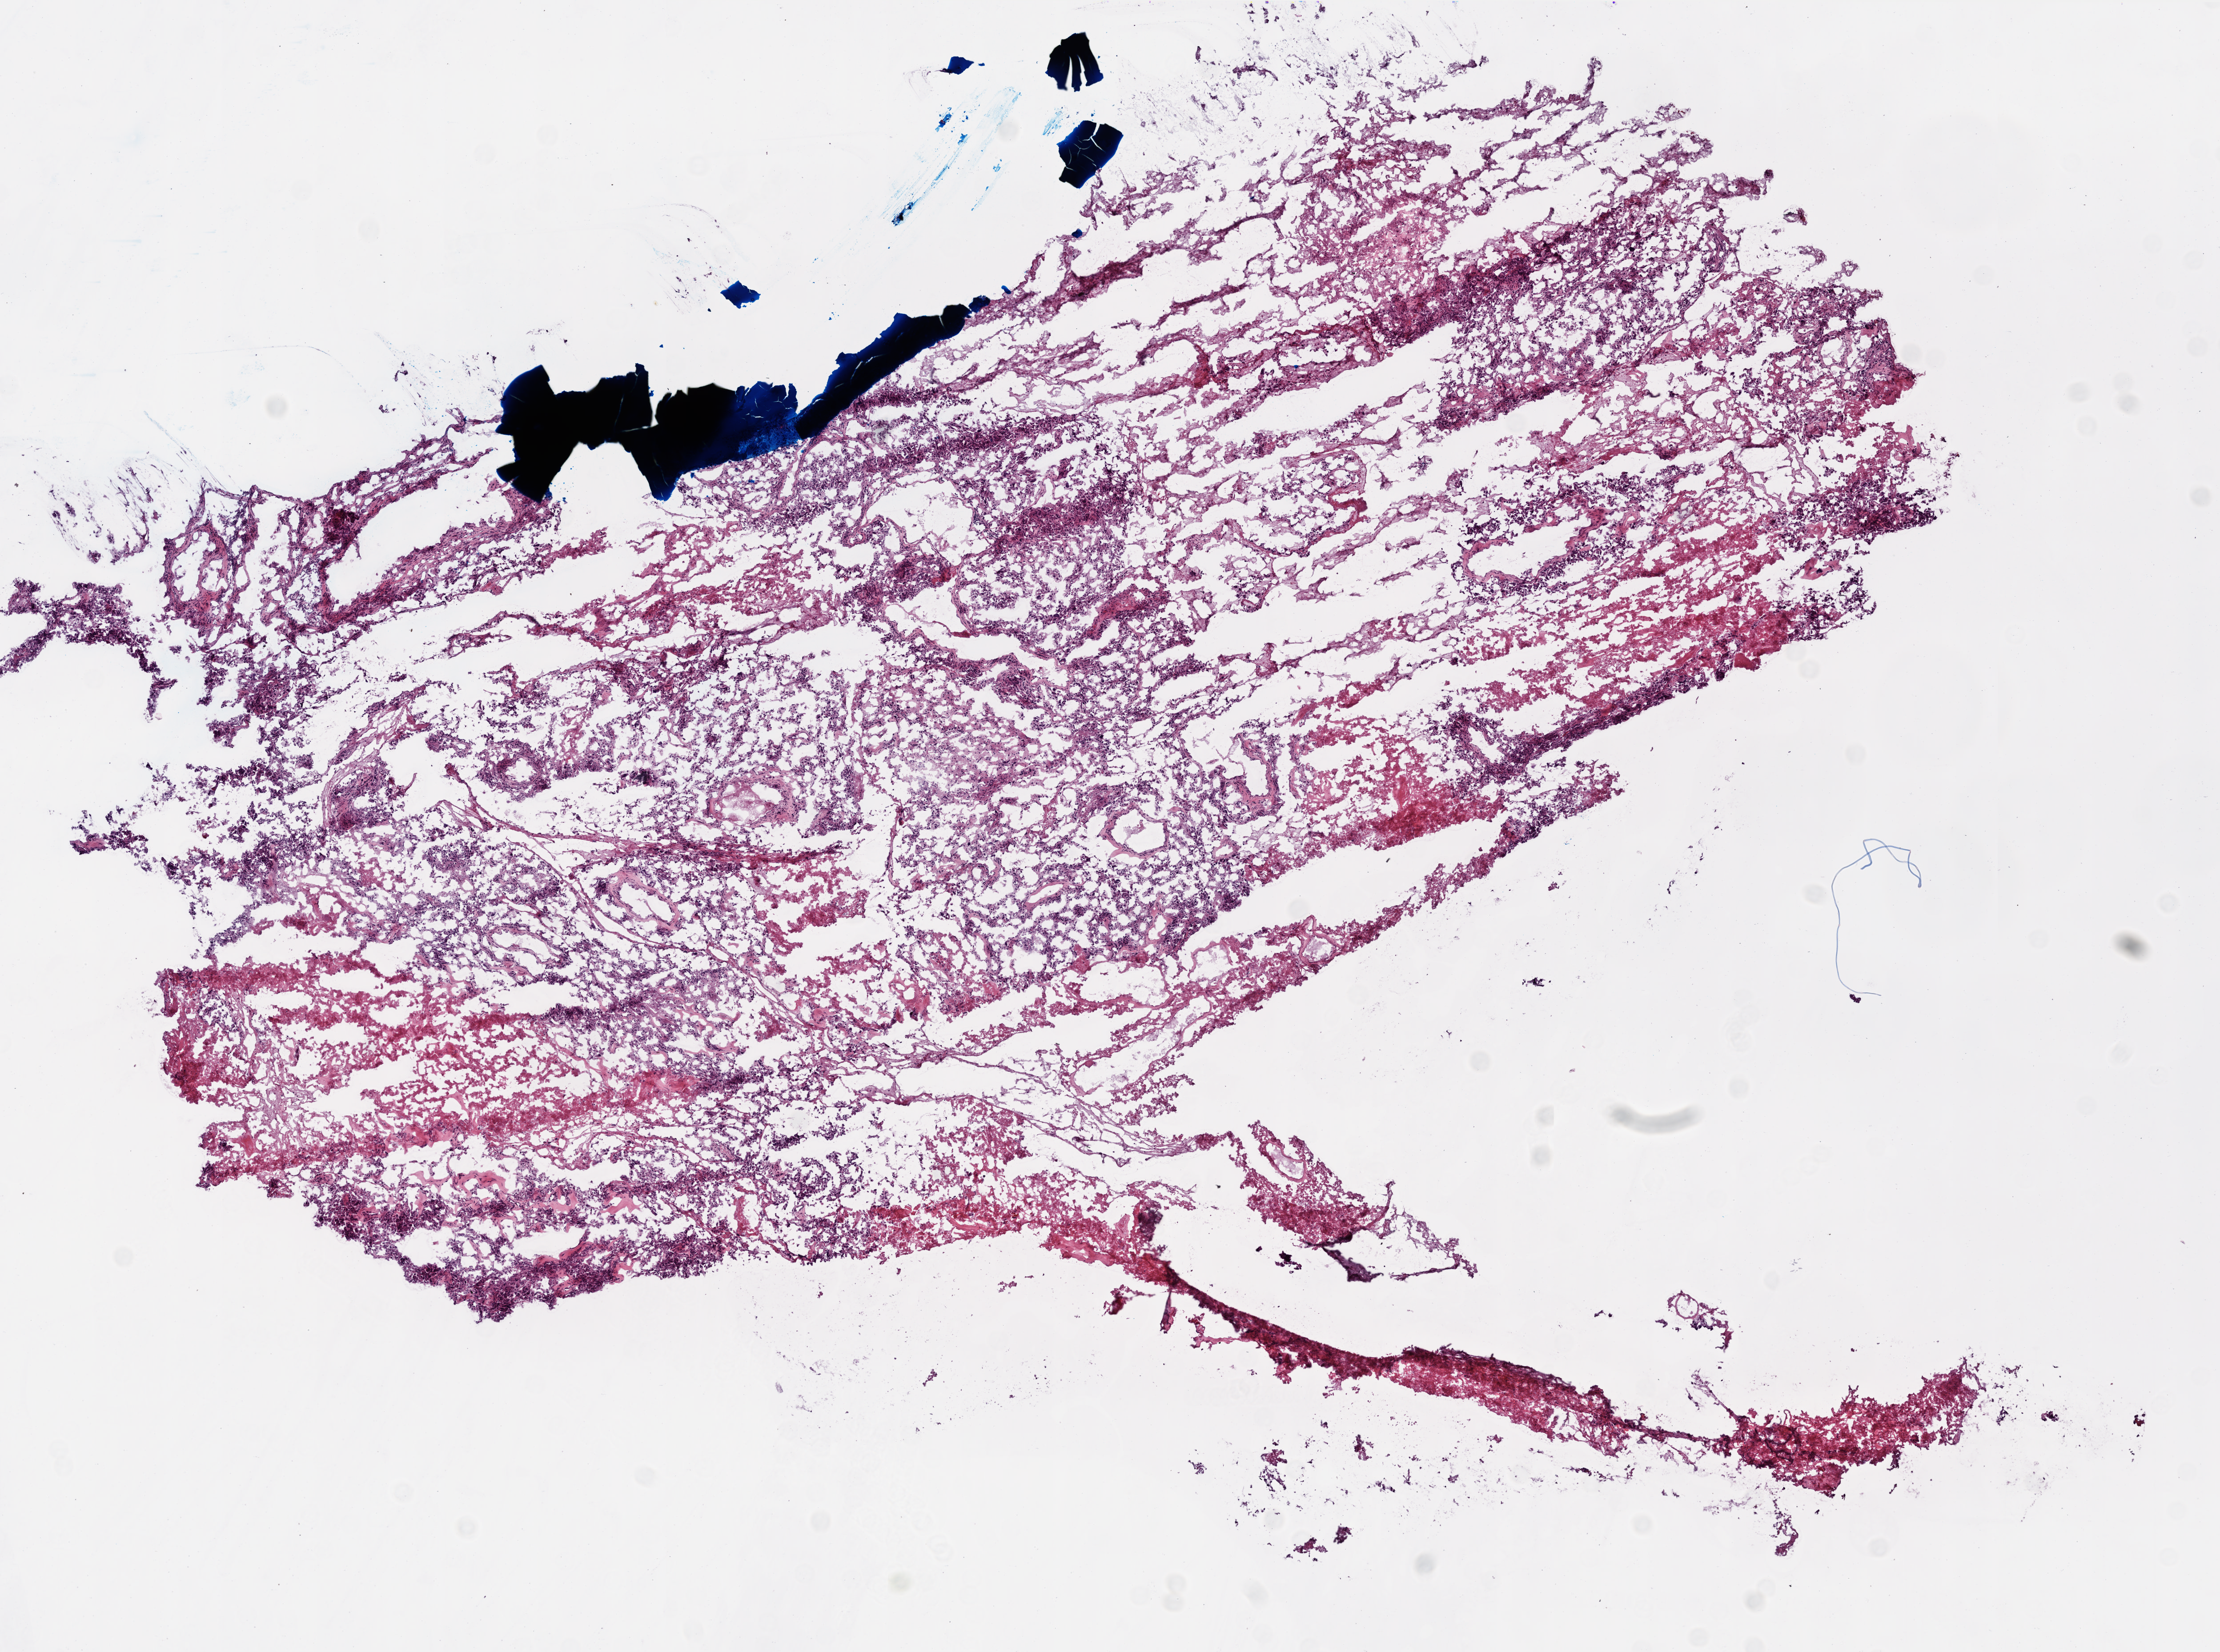
Digitized H&E-stained tissue section (whole slide) — a low-resolution overview of the entire scanned area, about 10.0 x 7.4 mm. Frozen section from the top of the tissue portion. Sample: primary tumour, brain. Patient: male, age at initial diagnosis 26 years.
Pathologic diagnosis: Glioblastoma.